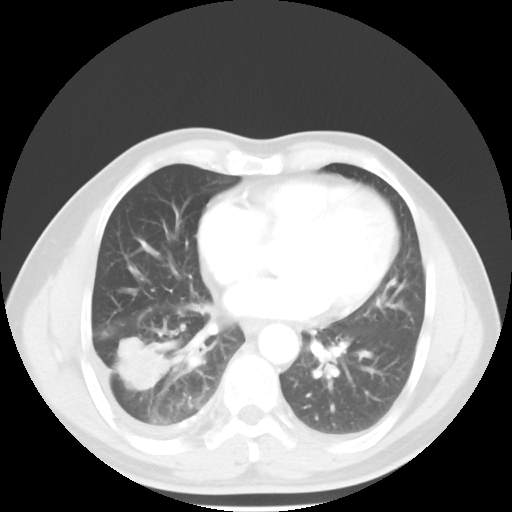
Chest CT, one axial slice; slice 23 of 56 in the series (ordered by position); reconstruction kernel STANDARD; lung window (W 1500 / L -600 HU); 5 mm slice thickness; 512 × 512 image matrix, field of view 344 × 344 mm. Male patient, age 56 years. Case-level facts recorded for this patient, not image findings: clinical TNM (as recorded): T2 N3 M1.
Annotated regions visible in this slice (bounding box drawn by a radiologist):
- lung tumour (recorded histology: adenocarcinoma): bounding box [x1, y1, x2, y2] px = [118, 334, 175, 399]